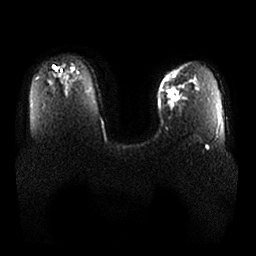
Breast MRI, one axial slice. Position 20 of 25 along the scan axis. Diffusion-weighted series; image 2 of 4 stored at this slice position (different b-values; order by instance number). 1.5 T. 4 mm slice thickness. 256 × 256 image matrix. Female patient.
Outlined on this slice (outlined manually by an expert reader):
- tumour on diffusion-weighted imaging: bounding box (x1, y1, x2, y2) in pixels: (165, 88, 180, 105)